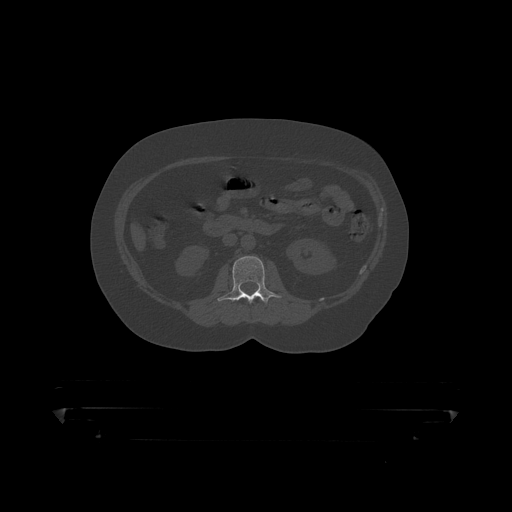
CT including the spine, one axial slice. Slice 120 of 390 in the series (ordered by position). 120 kVp. Bone window (W 1800 / L 400 HU). 1.25 mm slice thickness. 512 × 512 image matrix, field of view 650 × 650 mm. Male patient, age 60 years. From the clinical record (not read from this slice): primary cancer: prostate.
Structures marked on this image (semi-automatically segmented with operator editing):
- L2 vertebra: box from (x=218, y=256) to (x=282, y=306) px